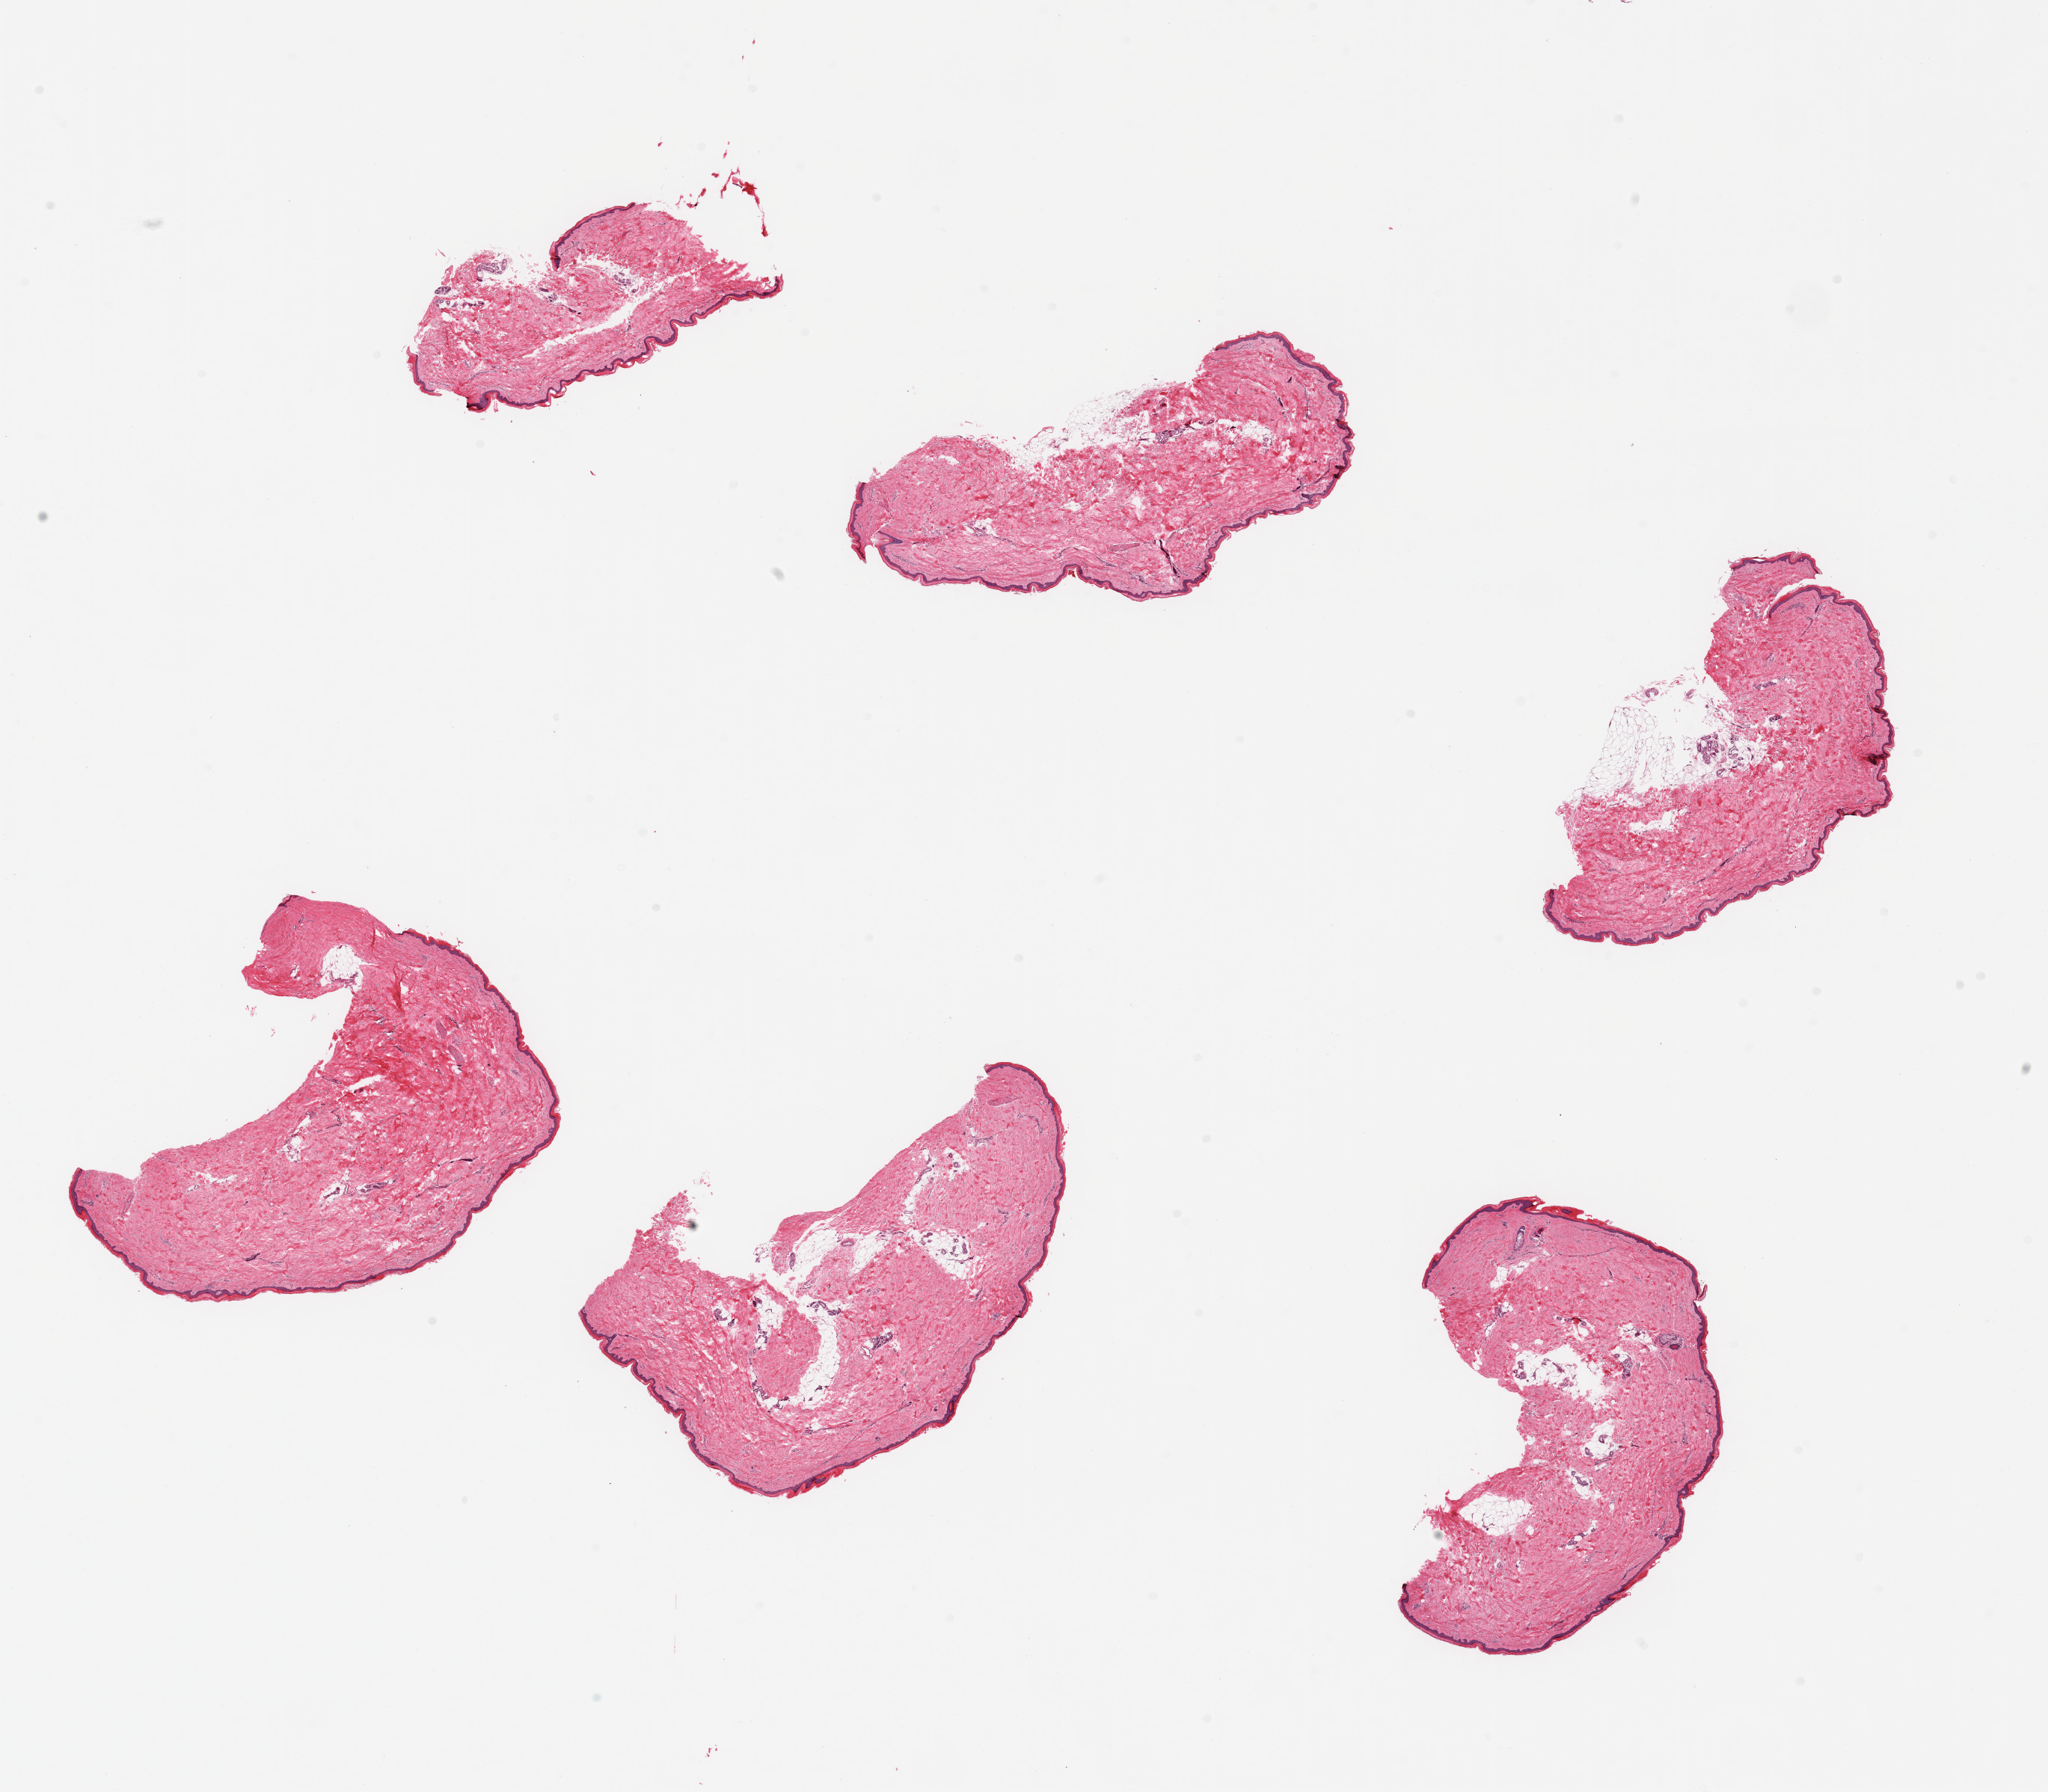
Digitized hematoxylin and eosin (H&E)-stained section, brightfield — whole scanned area (about 21.7 x 19.0 mm, acquisition: 20x scan) shown as a low-resolution overview, PAXgene-fixed paraffin-embedded (PFPE) section, sampled site (target tissue): skin of lower leg, donor tissue sample. Female donor.
Review note (as recorded): 6 pieces; well trimmed.